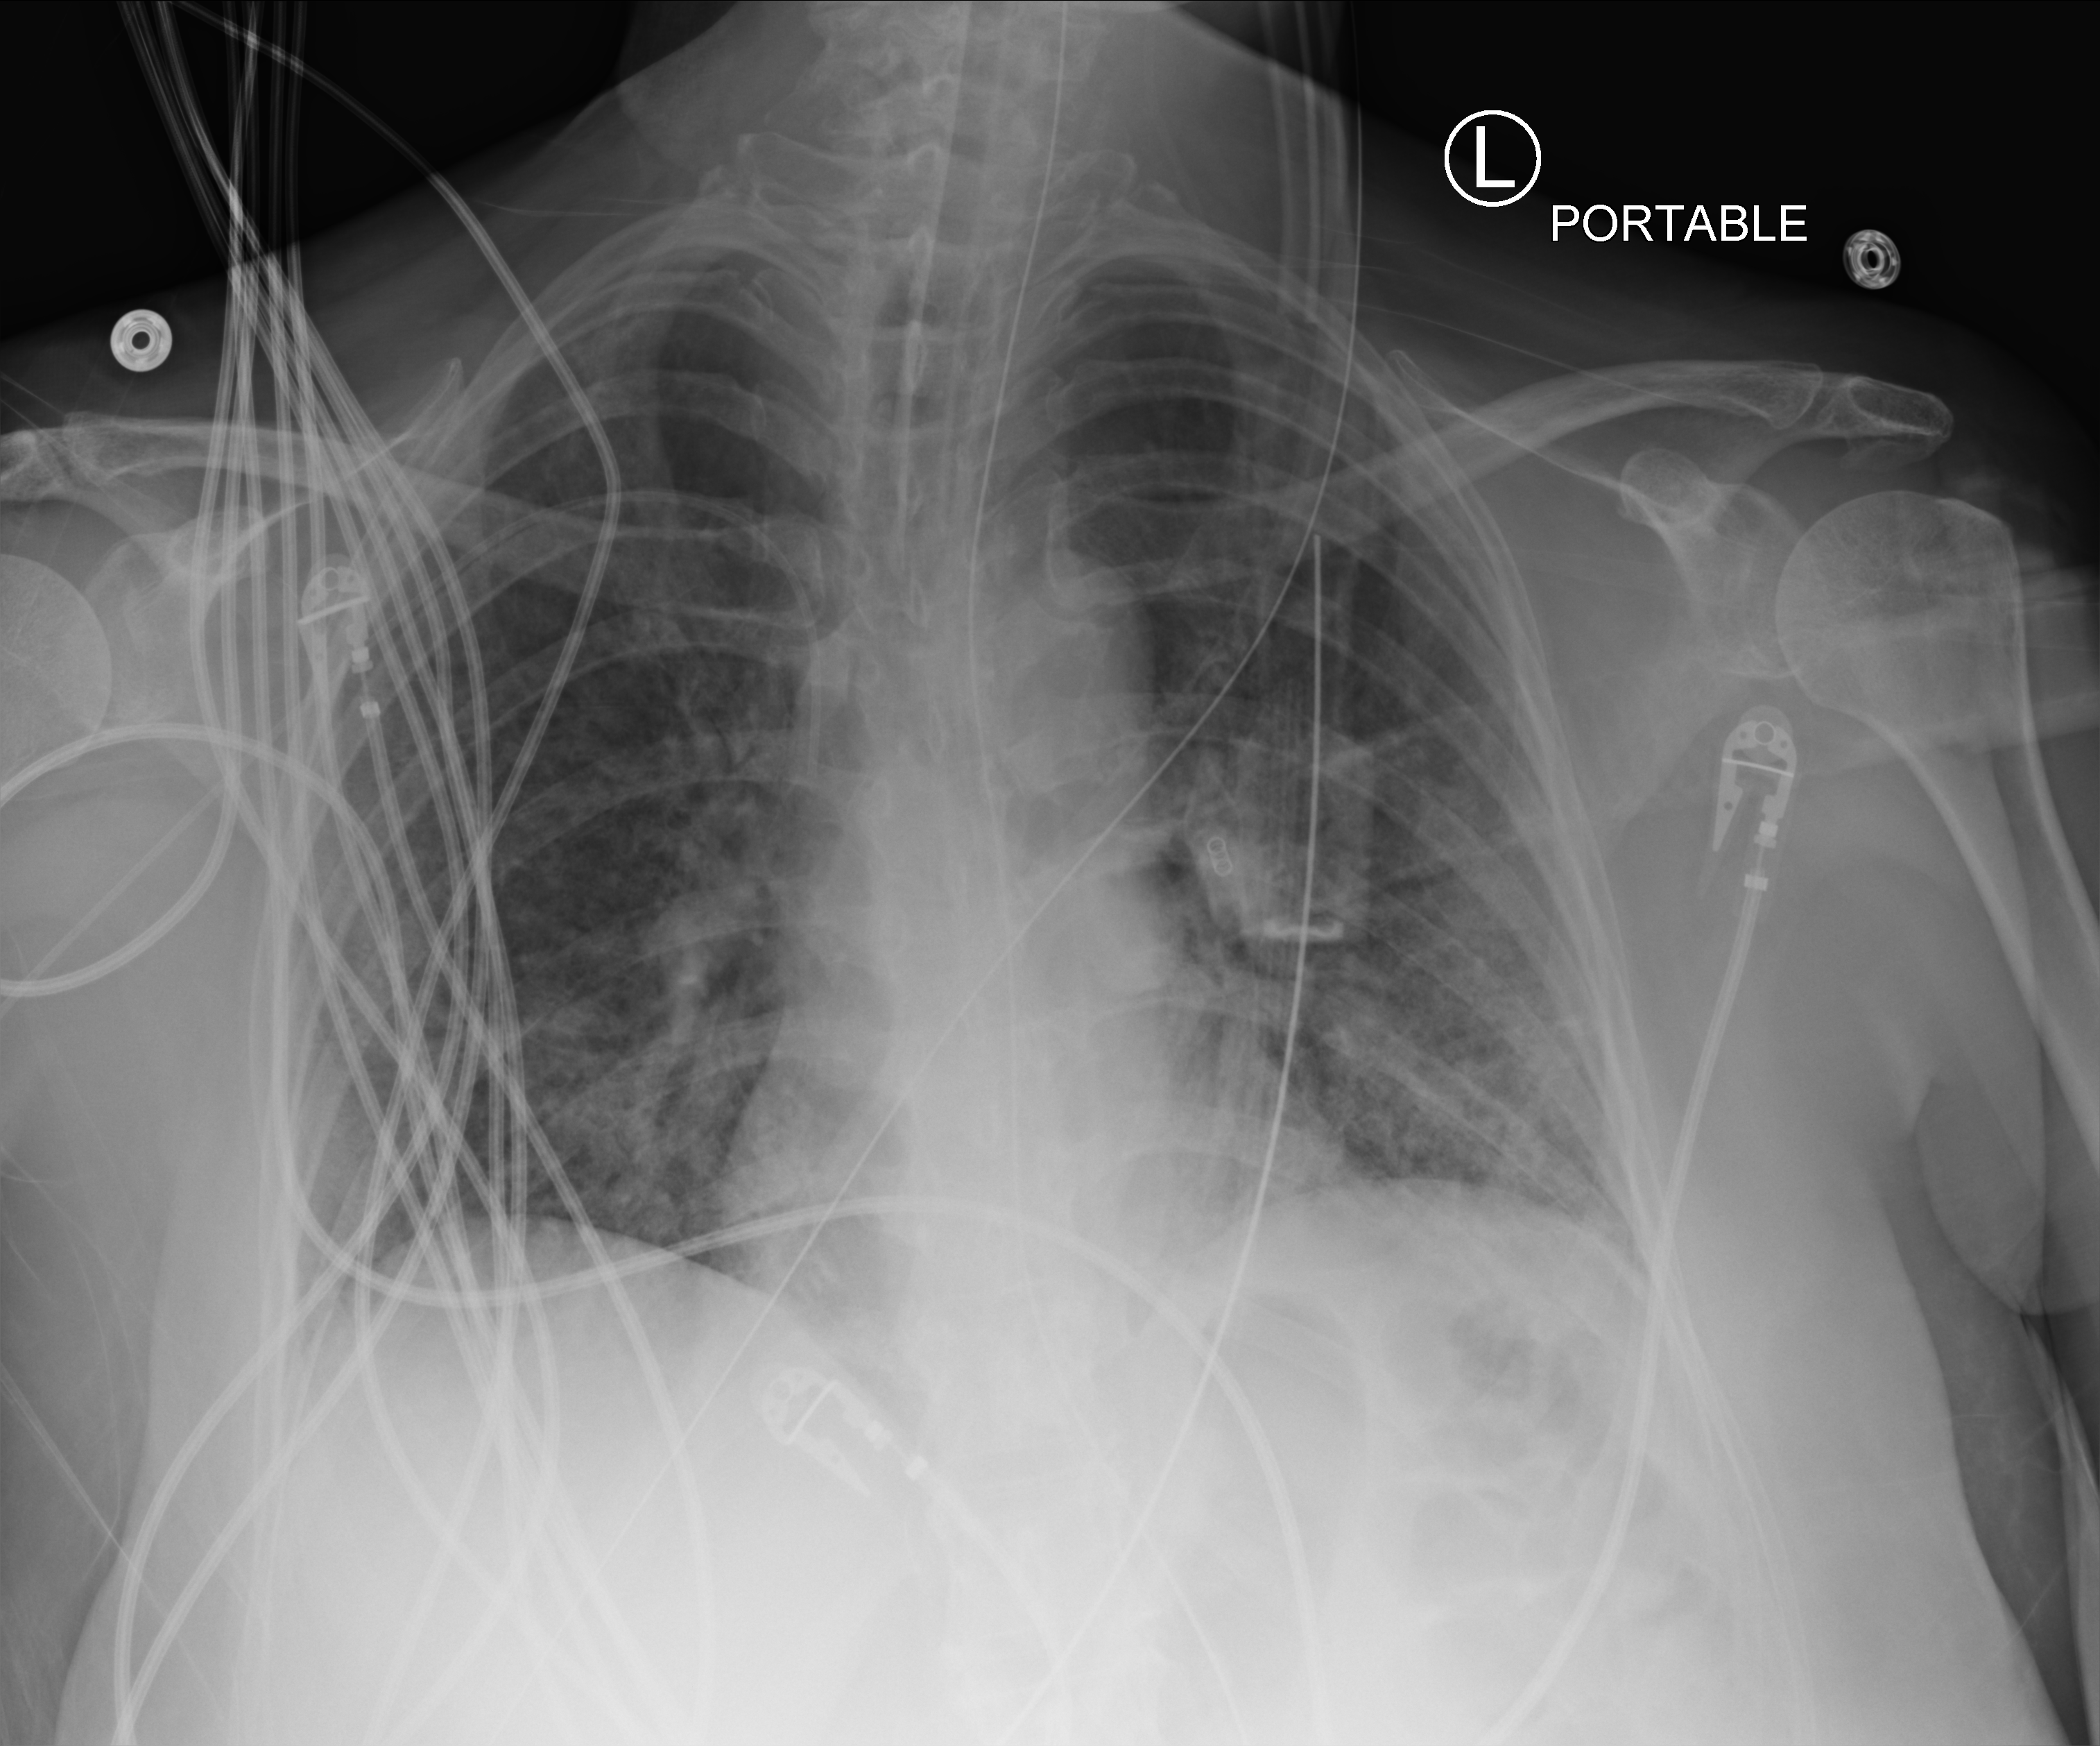
Bedside chest radiograph (computed radiography), anteroposterior (AP) projection. Female patient hospitalised with COVID-19, age 60–74 years.
From the hospital-stay record, not from the radiograph (when in the stay this image was taken is not recorded): mechanically ventilated during this hospital stay: yes.